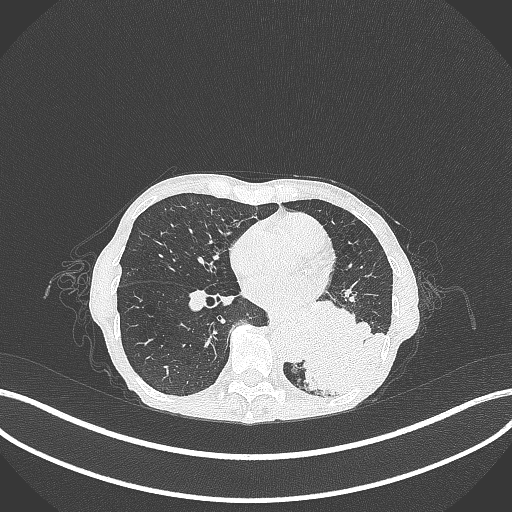
Chest CT, one axial slice; position 112 of 347 along the scan axis; reconstruction kernel B70f; 120 kVp; lung window (W 1500 / L -600 HU); 512 × 512 image matrix, field of view 400 × 400 mm. Female patient, age 70 years. Case-level facts recorded for this patient, not image findings: clinical TNM (as recorded): T3 N0 M0; histopathological grade: G3.
Structures marked on this image (rectangle marked by the reading radiologist):
- lung tumour (recorded histology: small cell carcinoma): bounding box [x1, y1, x2, y2] px = [293, 308, 389, 398]